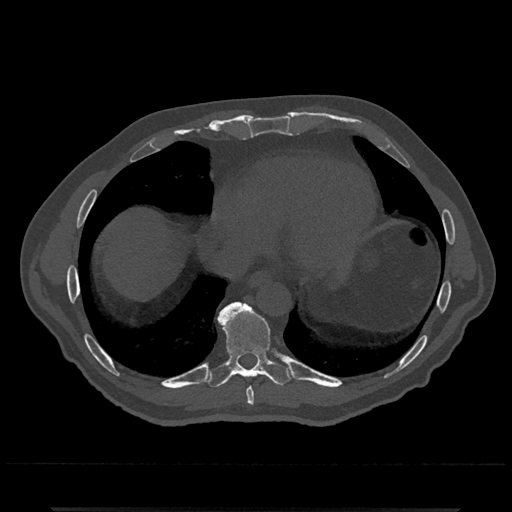
CT including the spine, one axial slice; slice 624 of 797 in the series (ordered by position); bone window (W 1800 / L 400 HU); 0.5 mm slice thickness; 512 × 512 image matrix, field of view 393 × 393 mm. Male patient, age 67 years. Case-level facts recorded for this patient, not image findings: primary cancer: prostate.
Structures marked on this image (semi-automatic segmentation, software-assisted and operator-edited):
- T8 vertebra: bounding box [x1, y1, x2, y2] px = [246, 387, 254, 406]
- T9 vertebra: [205, 302, 293, 388]